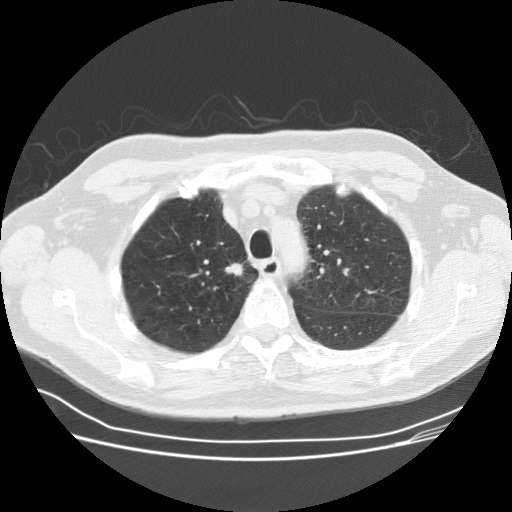
Low-dose screening chest CT, one axial slice. Position 125 of 164 along the scan axis. Reconstruction kernel STANDARD. 120 kVp. Lung window (W 1500 / L -600 HU). 2.5 mm slice thickness. 512 × 512 image matrix, field of view 360 × 360 mm.
Structures marked on this image (expert manual segmentation):
- lesion 1 (tumor, upper lobe of right lung): bounding box [x1, y1, x2, y2] px = [225, 263, 243, 276]